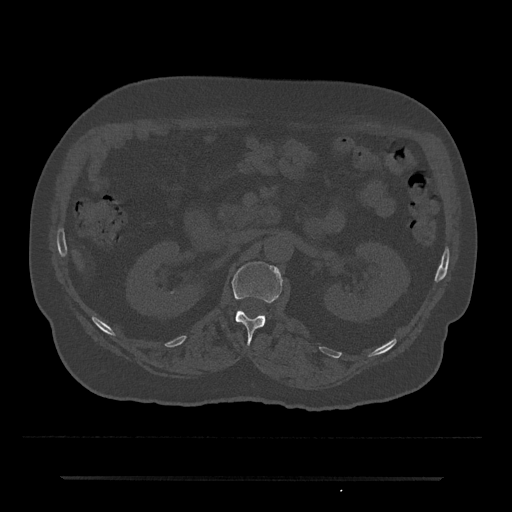
CT including the spine, one axial slice; slice 63 of 797 in the series (ordered by position); reconstruction kernel Br40s/3; 120 kVp; bone window (W 1800 / L 400 HU); 0.5 mm slice thickness; 512 × 512 image matrix, field of view 437 × 437 mm. Patient: male, 69 years. Case-level facts recorded for this patient, not image findings: primary cancer: prostate.
Structures marked on this image (semi-automatically segmented with operator editing):
- L1 vertebra: bounding box (x1, y1, x2, y2) in pixels: (232, 262, 282, 342)